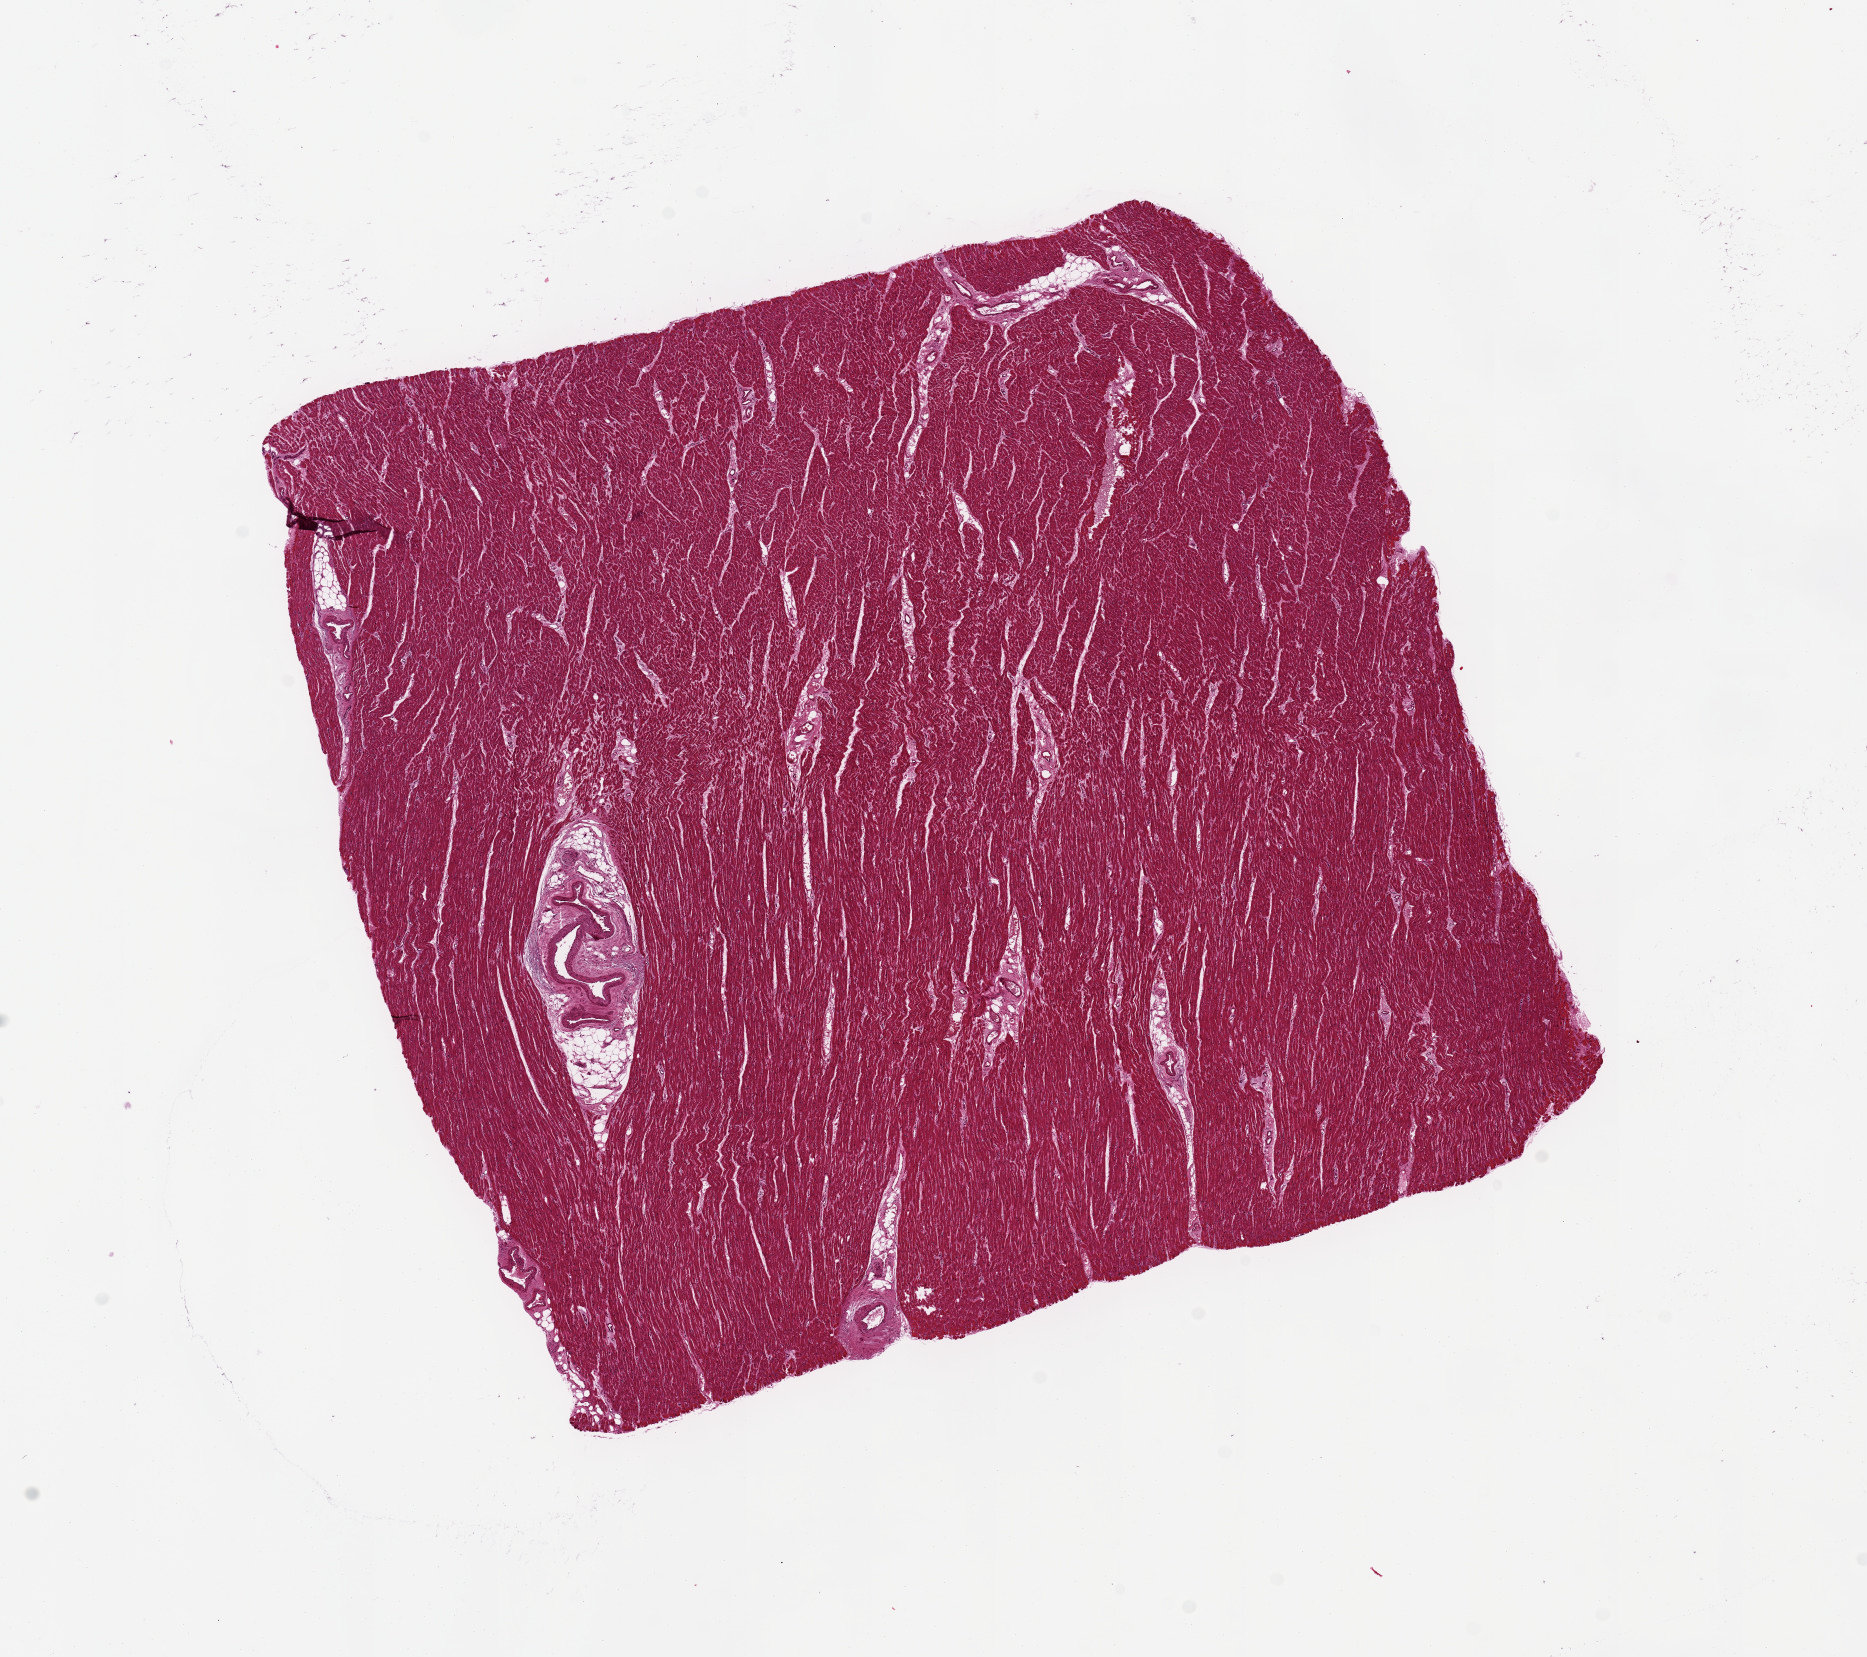
Digitized haematoxylin and eosin-stained section, a low-resolution overview of the entire scanned area, about 14.8 x 13.1 mm (acquisition: 20x scan), PAXgene-fixed, paraffin-embedded tissue, target tissue: heart, donor tissue sample.
- pathologist's review note for this sample: 9x8 mm